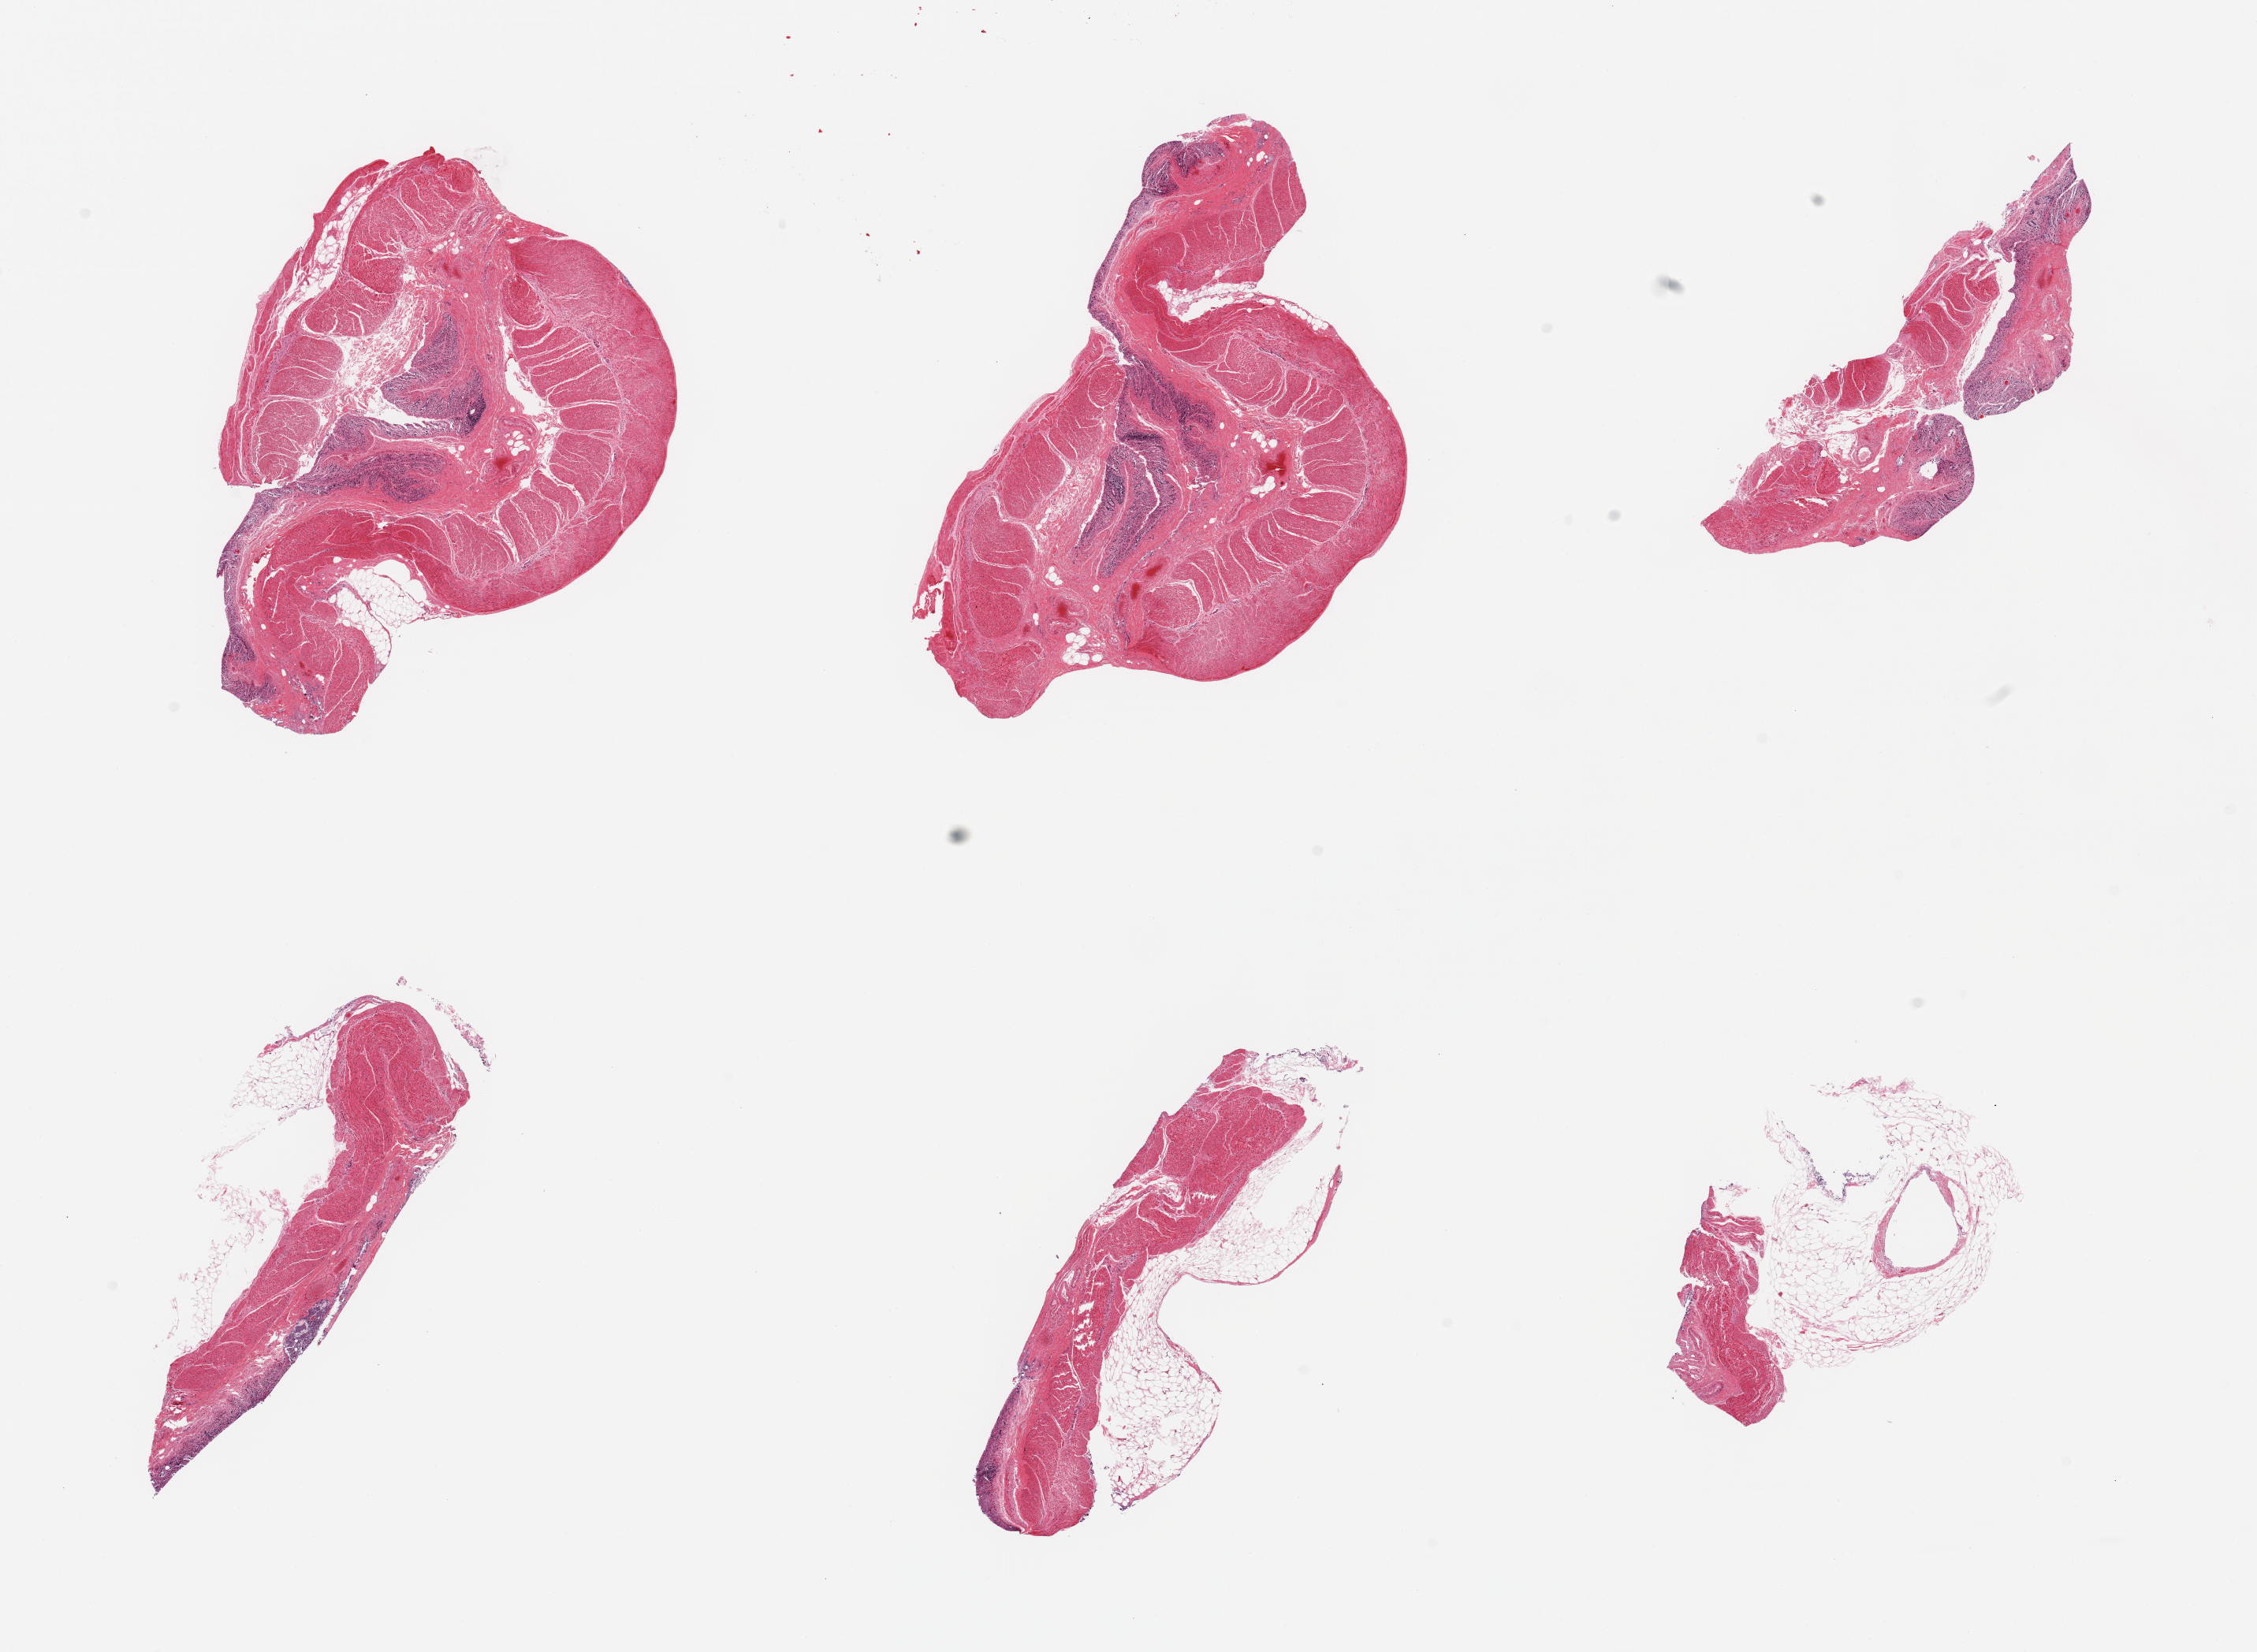
Haematoxylin and eosin whole-slide image — low-resolution overview of the scanned area, about 22.6 x 16.6 mm, PAXgene-fixed paraffin-embedded (PFPE) section, target tissue: transverse colon, tissue donor sample. Female donor.
Pathologist's review note for this sample: 6 pieces; mucosa autolyzed or absent; muscle intact.